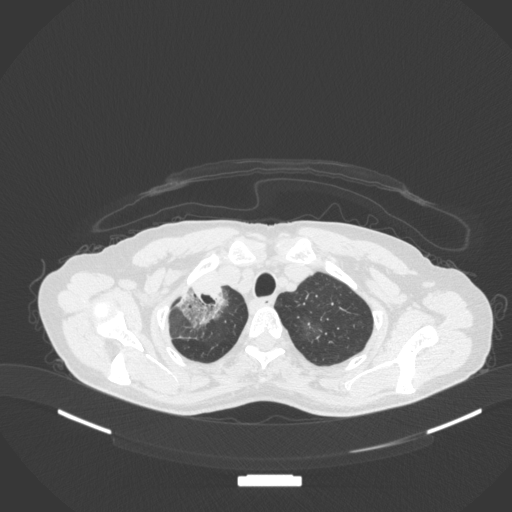
Chest CT, one axial slice; position 283 of 311 along the scan axis; reconstruction kernel B31f; 120 kVp; lung window (W 1500 / L -600 HU); 1 mm slice thickness; 512 × 512 image matrix, field of view 400 × 400 mm. Patient: female, 59 years. From the clinical record (not read from this slice): clinical TNM (as recorded): T3 N0 M0; histopathological grade: G1.
Structures marked on this image (bounding box drawn by a radiologist):
- lung tumour (recorded histology: adenocarcinoma): bounding box [x1, y1, x2, y2] px = [174, 284, 228, 336]